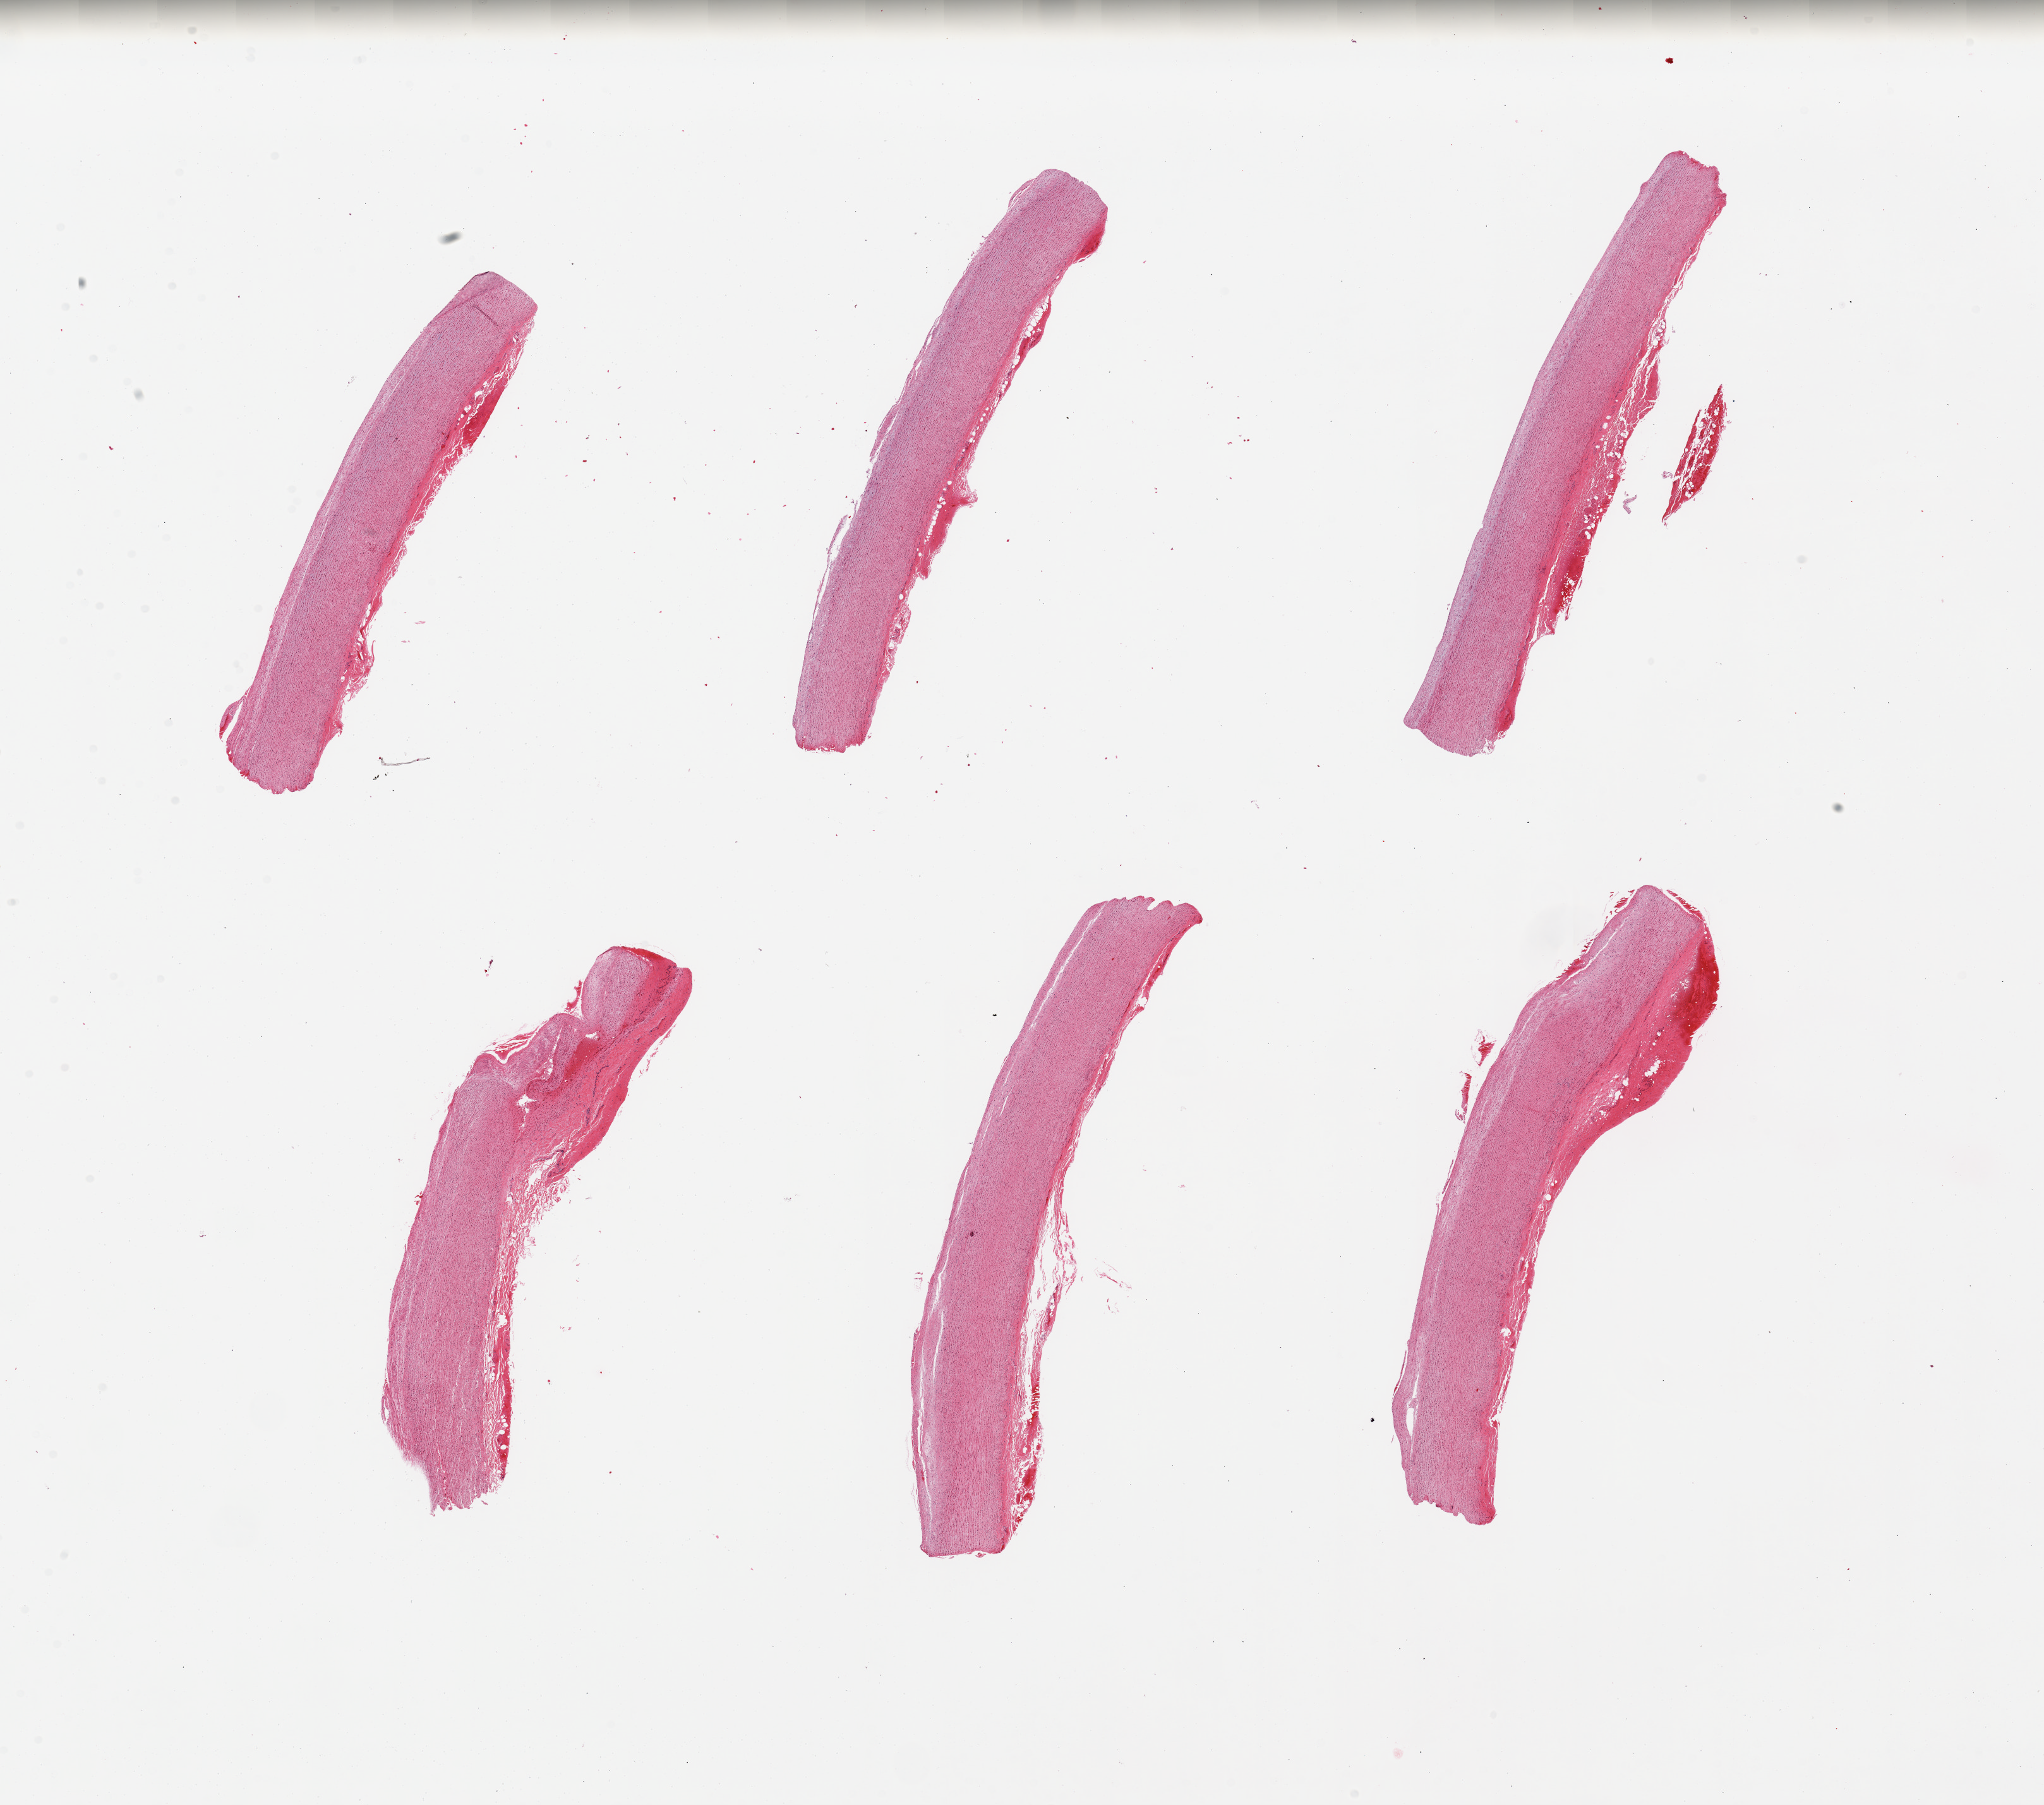
Whole-slide image, hematoxylin and eosin (H&E) stain — a low-resolution overview of the entire scanned area, about 25.6 x 22.6 mm. PAXgene-fixed, paraffin-embedded tissue. Section of aorta (target tissue). Tissue donor sample. Male donor.
* pathologist's review note for this sample: 6 pieces. Minimal plaques